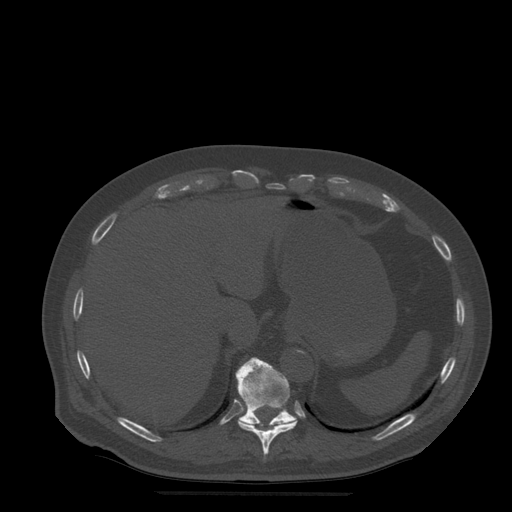
CT including the spine, one axial slice; slice 258 of 522 in the series (ordered by position); bone window (W 1800 / L 400 HU); 512 × 512 image matrix, field of view 420 × 420 mm. Patient age 72 years. From the clinical record (not read from this slice): primary cancer: prostate.
Structures marked on this image (semi-automatic segmentation, software-assisted and operator-edited):
- T10 vertebra: bounding box <238,419,297,455> (left, top, right, bottom; pixels)
- T11 vertebra: <236,358,298,426>